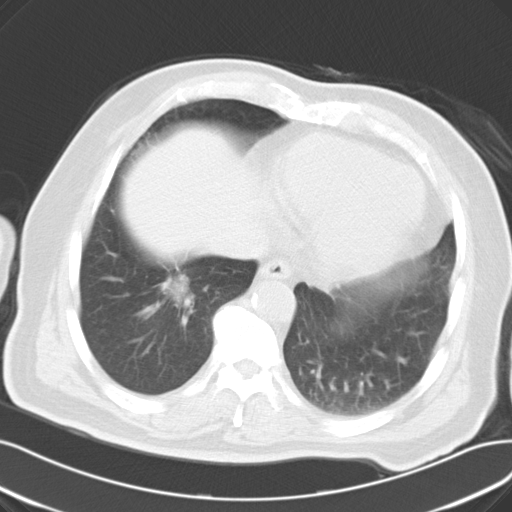
Chest CT, one axial slice; position 12 of 30 along the scan axis; 120 kVp; lung window (W 1500 / L -600 HU); 10 mm slice thickness; 512 × 512 image matrix, field of view 363 × 363 mm. Patient: male, 69 years. Case-level facts recorded for this patient, not image findings: clinical TNM (as recorded): T1c N0 M0.
Annotated regions visible in this slice (bounding box drawn by a radiologist):
- lung tumour (recorded histology: adenocarcinoma): bounding box (x1, y1, x2, y2) in pixels: (153, 268, 195, 312)